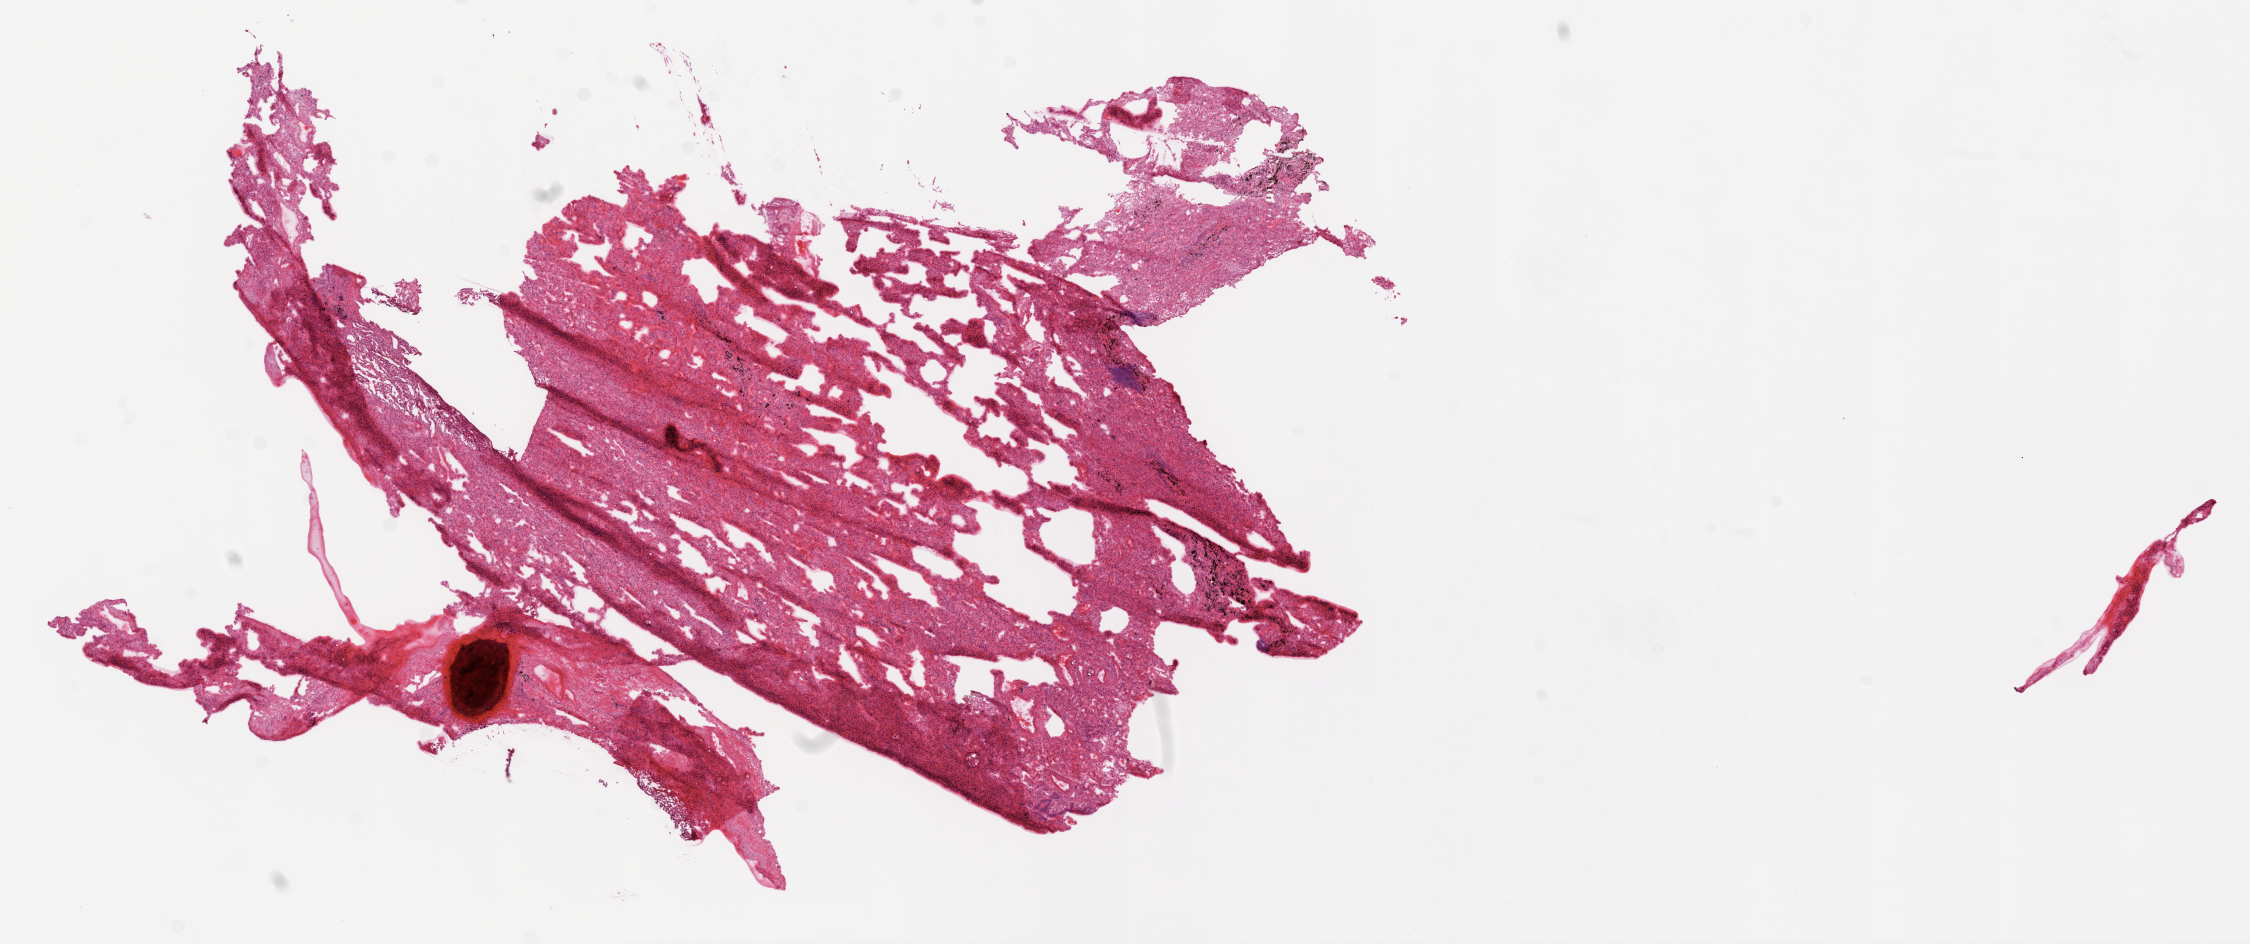
H&E-stained whole-slide image — whole scanned area (about 18.1 x 7.6 mm) shown as a low-resolution overview; frozen section; lung, solid tissue normal (non-tumour tissue) sample. Male, age 79 years at initial diagnosis.
* this section: solid tissue normal sample (biorepository sample class)
* patient diagnosis: Squamous cell carcinoma, NOS (lower lobe, lung)